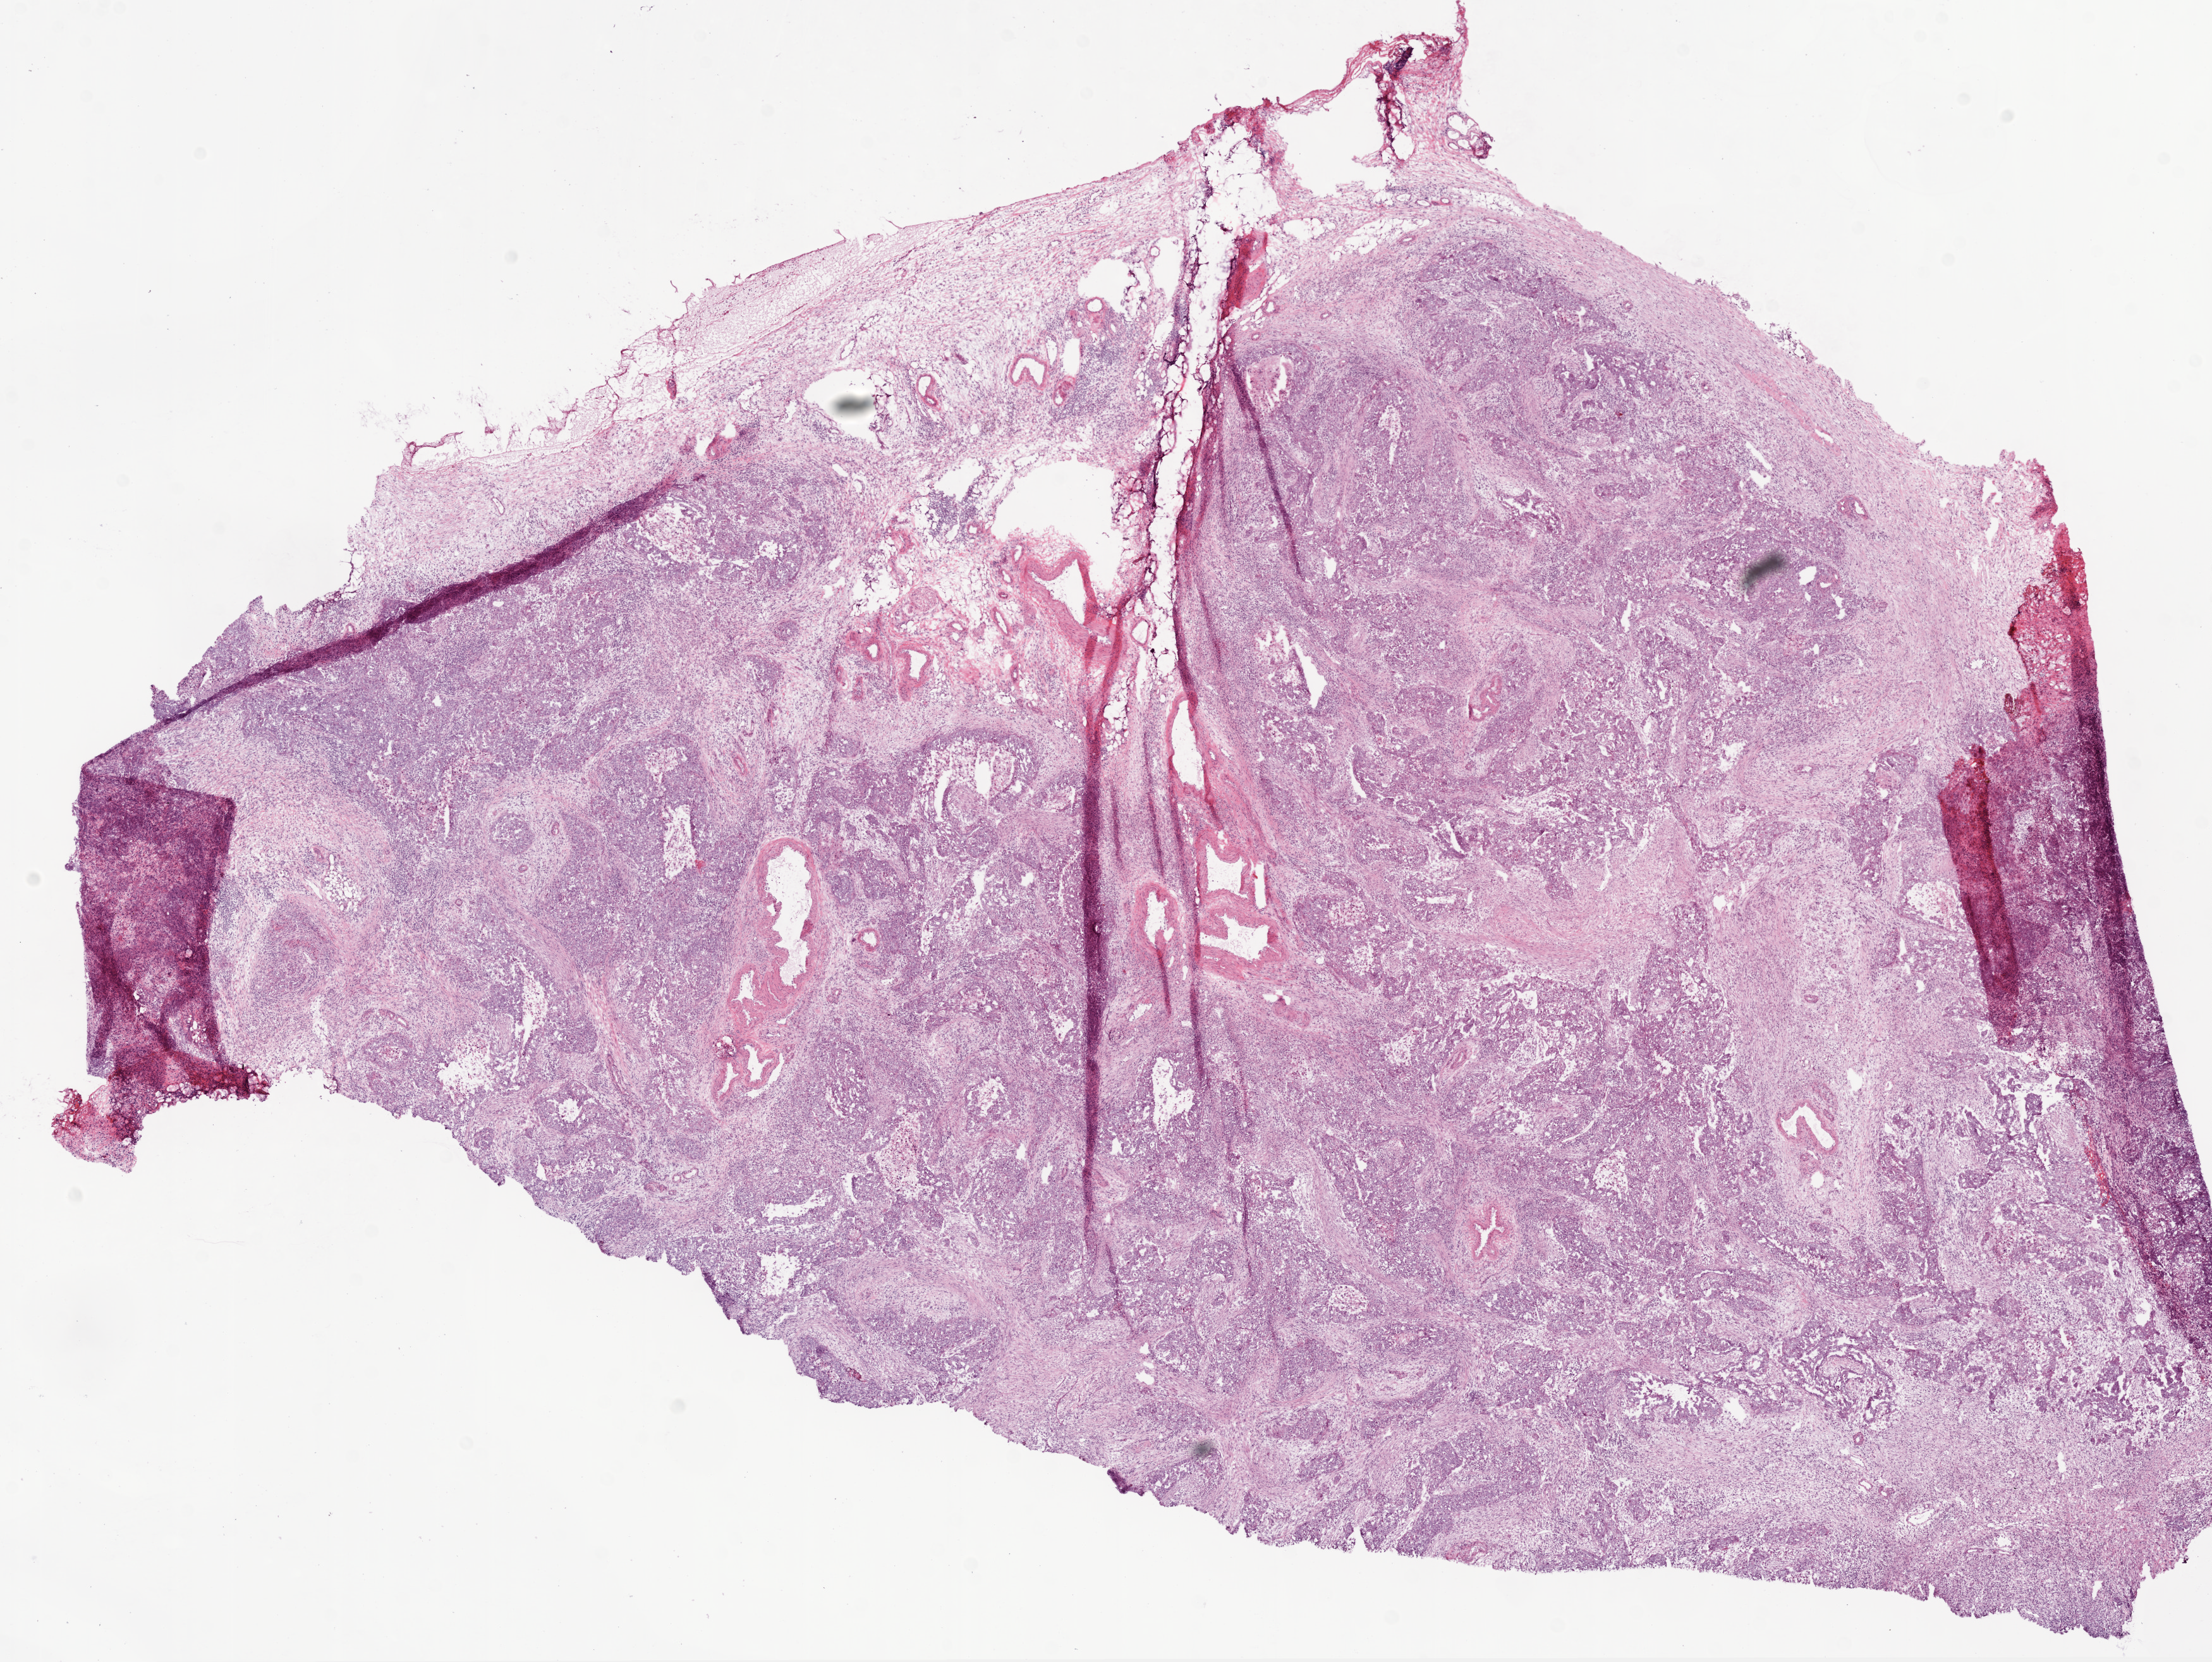
Digitized H&E-stained tissue section (whole slide) — whole scanned area (about 14.0 x 10.5 mm) shown as a low-resolution overview; frozen section from the bottom of the tissue portion; primary tumour sample from the ovary. Female patient; age at initial diagnosis 71 years. Pathologist review of this section (percent, as recorded): tumour cells 70%, tumour nuclei 80%.
Pathologic diagnosis: Serous cystadenocarcinoma, NOS.